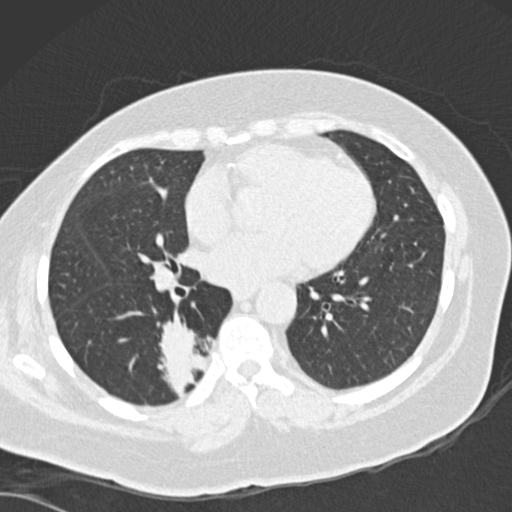
Low-dose screening chest CT, one axial slice; position 70 of 162 along the scan axis; 120 kVp; lung window (W 1500 / L -600 HU); 2 mm slice thickness; 512 × 512 image matrix, field of view 328 × 328 mm.
Annotated regions visible in this slice (outlined manually by an expert reader):
- lesion 1 (tumor, lower lobe of right lung): bounding box (x1, y1, x2, y2) in pixels: (158, 308, 214, 396)